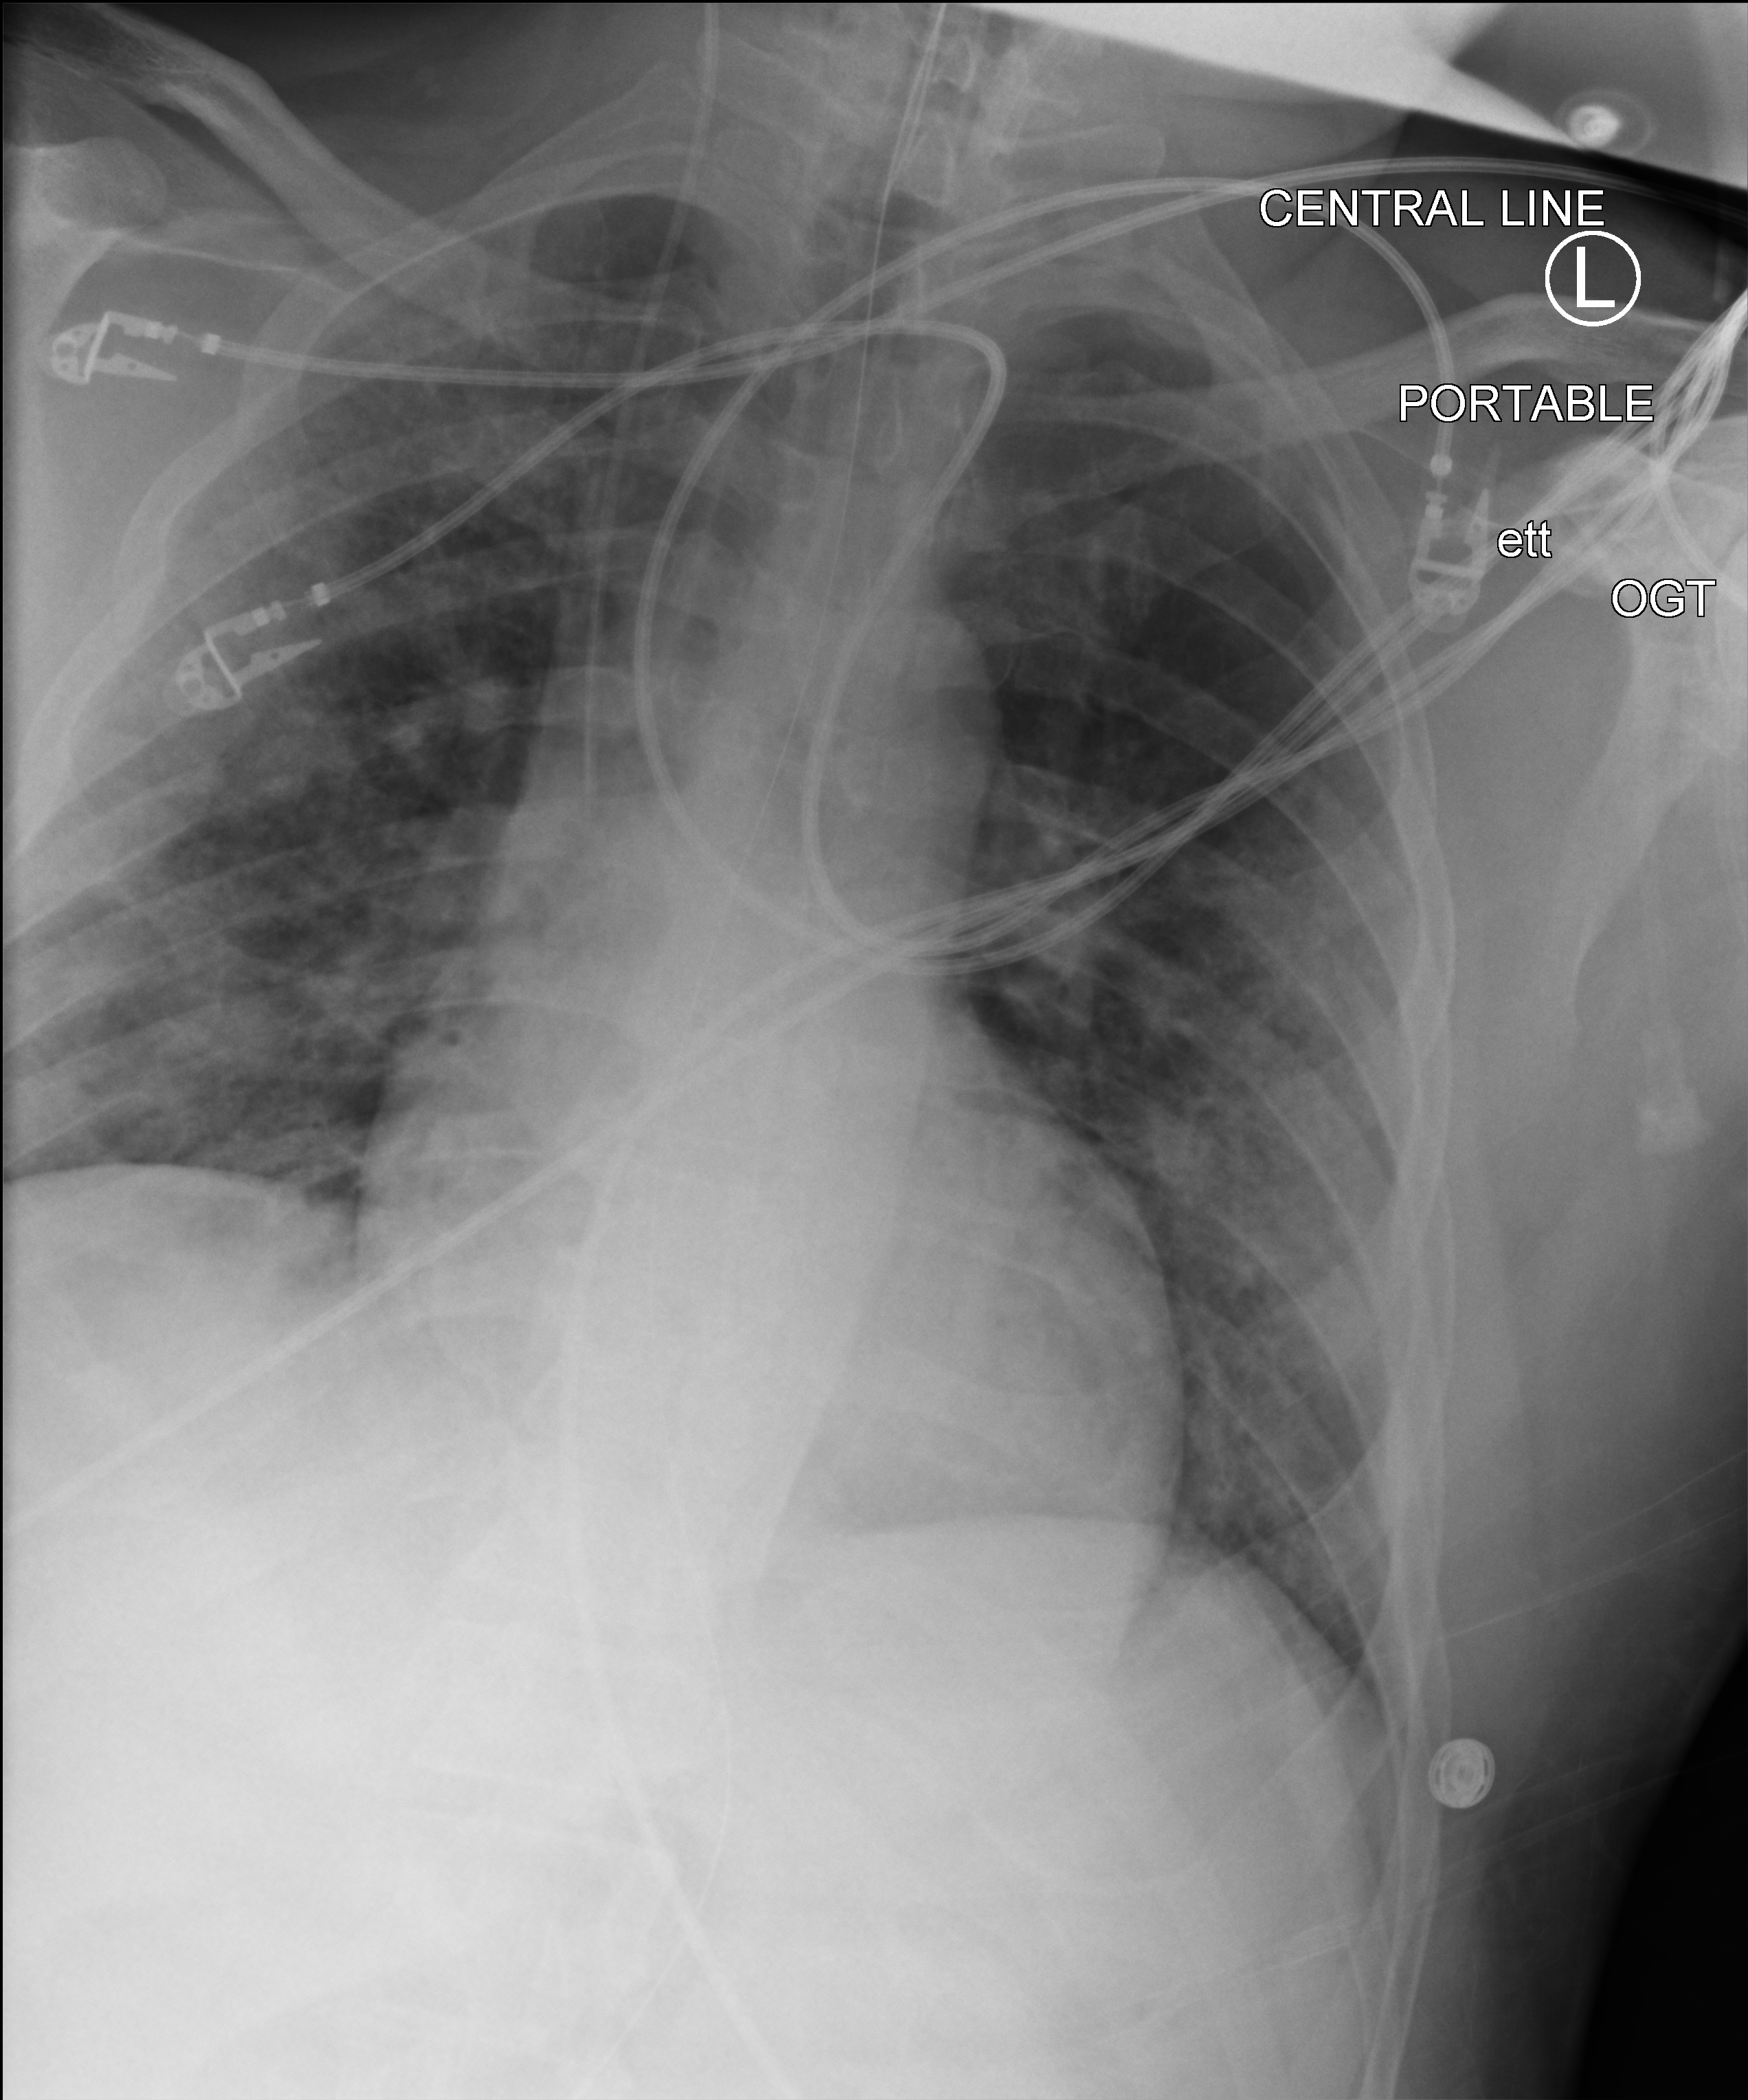
Bedside chest radiograph (computed radiography), anteroposterior (AP) projection. Male patient hospitalised with COVID-19, age 18–59 years.
From the hospital-stay record, not from the radiograph (when in the stay this image was taken is not recorded):
- mechanically ventilated during this hospital stay: yes
- admitted to intensive care during this hospital stay: no